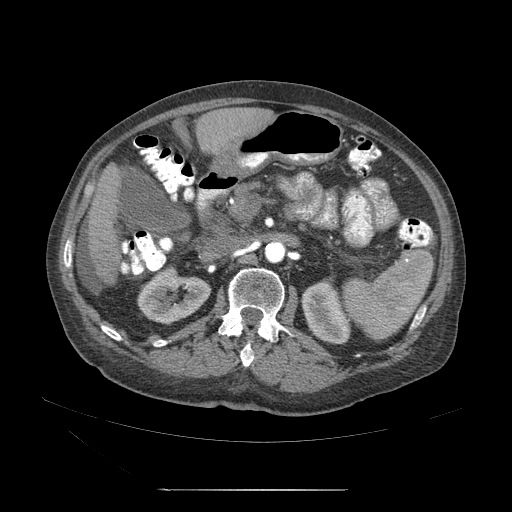
Contrast-enhanced abdominal CT (liver protocol), one axial slice; slice 16 of 71 in the series (ordered by position); 120 kVp; soft-tissue window (W 400 / L 40 HU); 2.5 mm slice thickness; 512 × 512 image matrix. From the clinical record (not read from this slice): diagnosis: hepatocellular carcinoma (patient treated with transarterial chemoembolisation; whether this scan precedes or follows treatment is not stated here); TNM stage (as recorded): Stage-II; Child-Pugh class: A; tumour nodularity: multinodular; tumour size: 1 cm.
Structures marked on this image (semi-automatically segmented with operator editing):
- abdominal aorta: bounding box (x1, y1, x2, y2) in pixels: (265, 242, 287, 265)
- liver parenchyma outside the tumour (the mass and vessels are separate outlines, so this box may not span the whole liver): (102, 182, 128, 249)